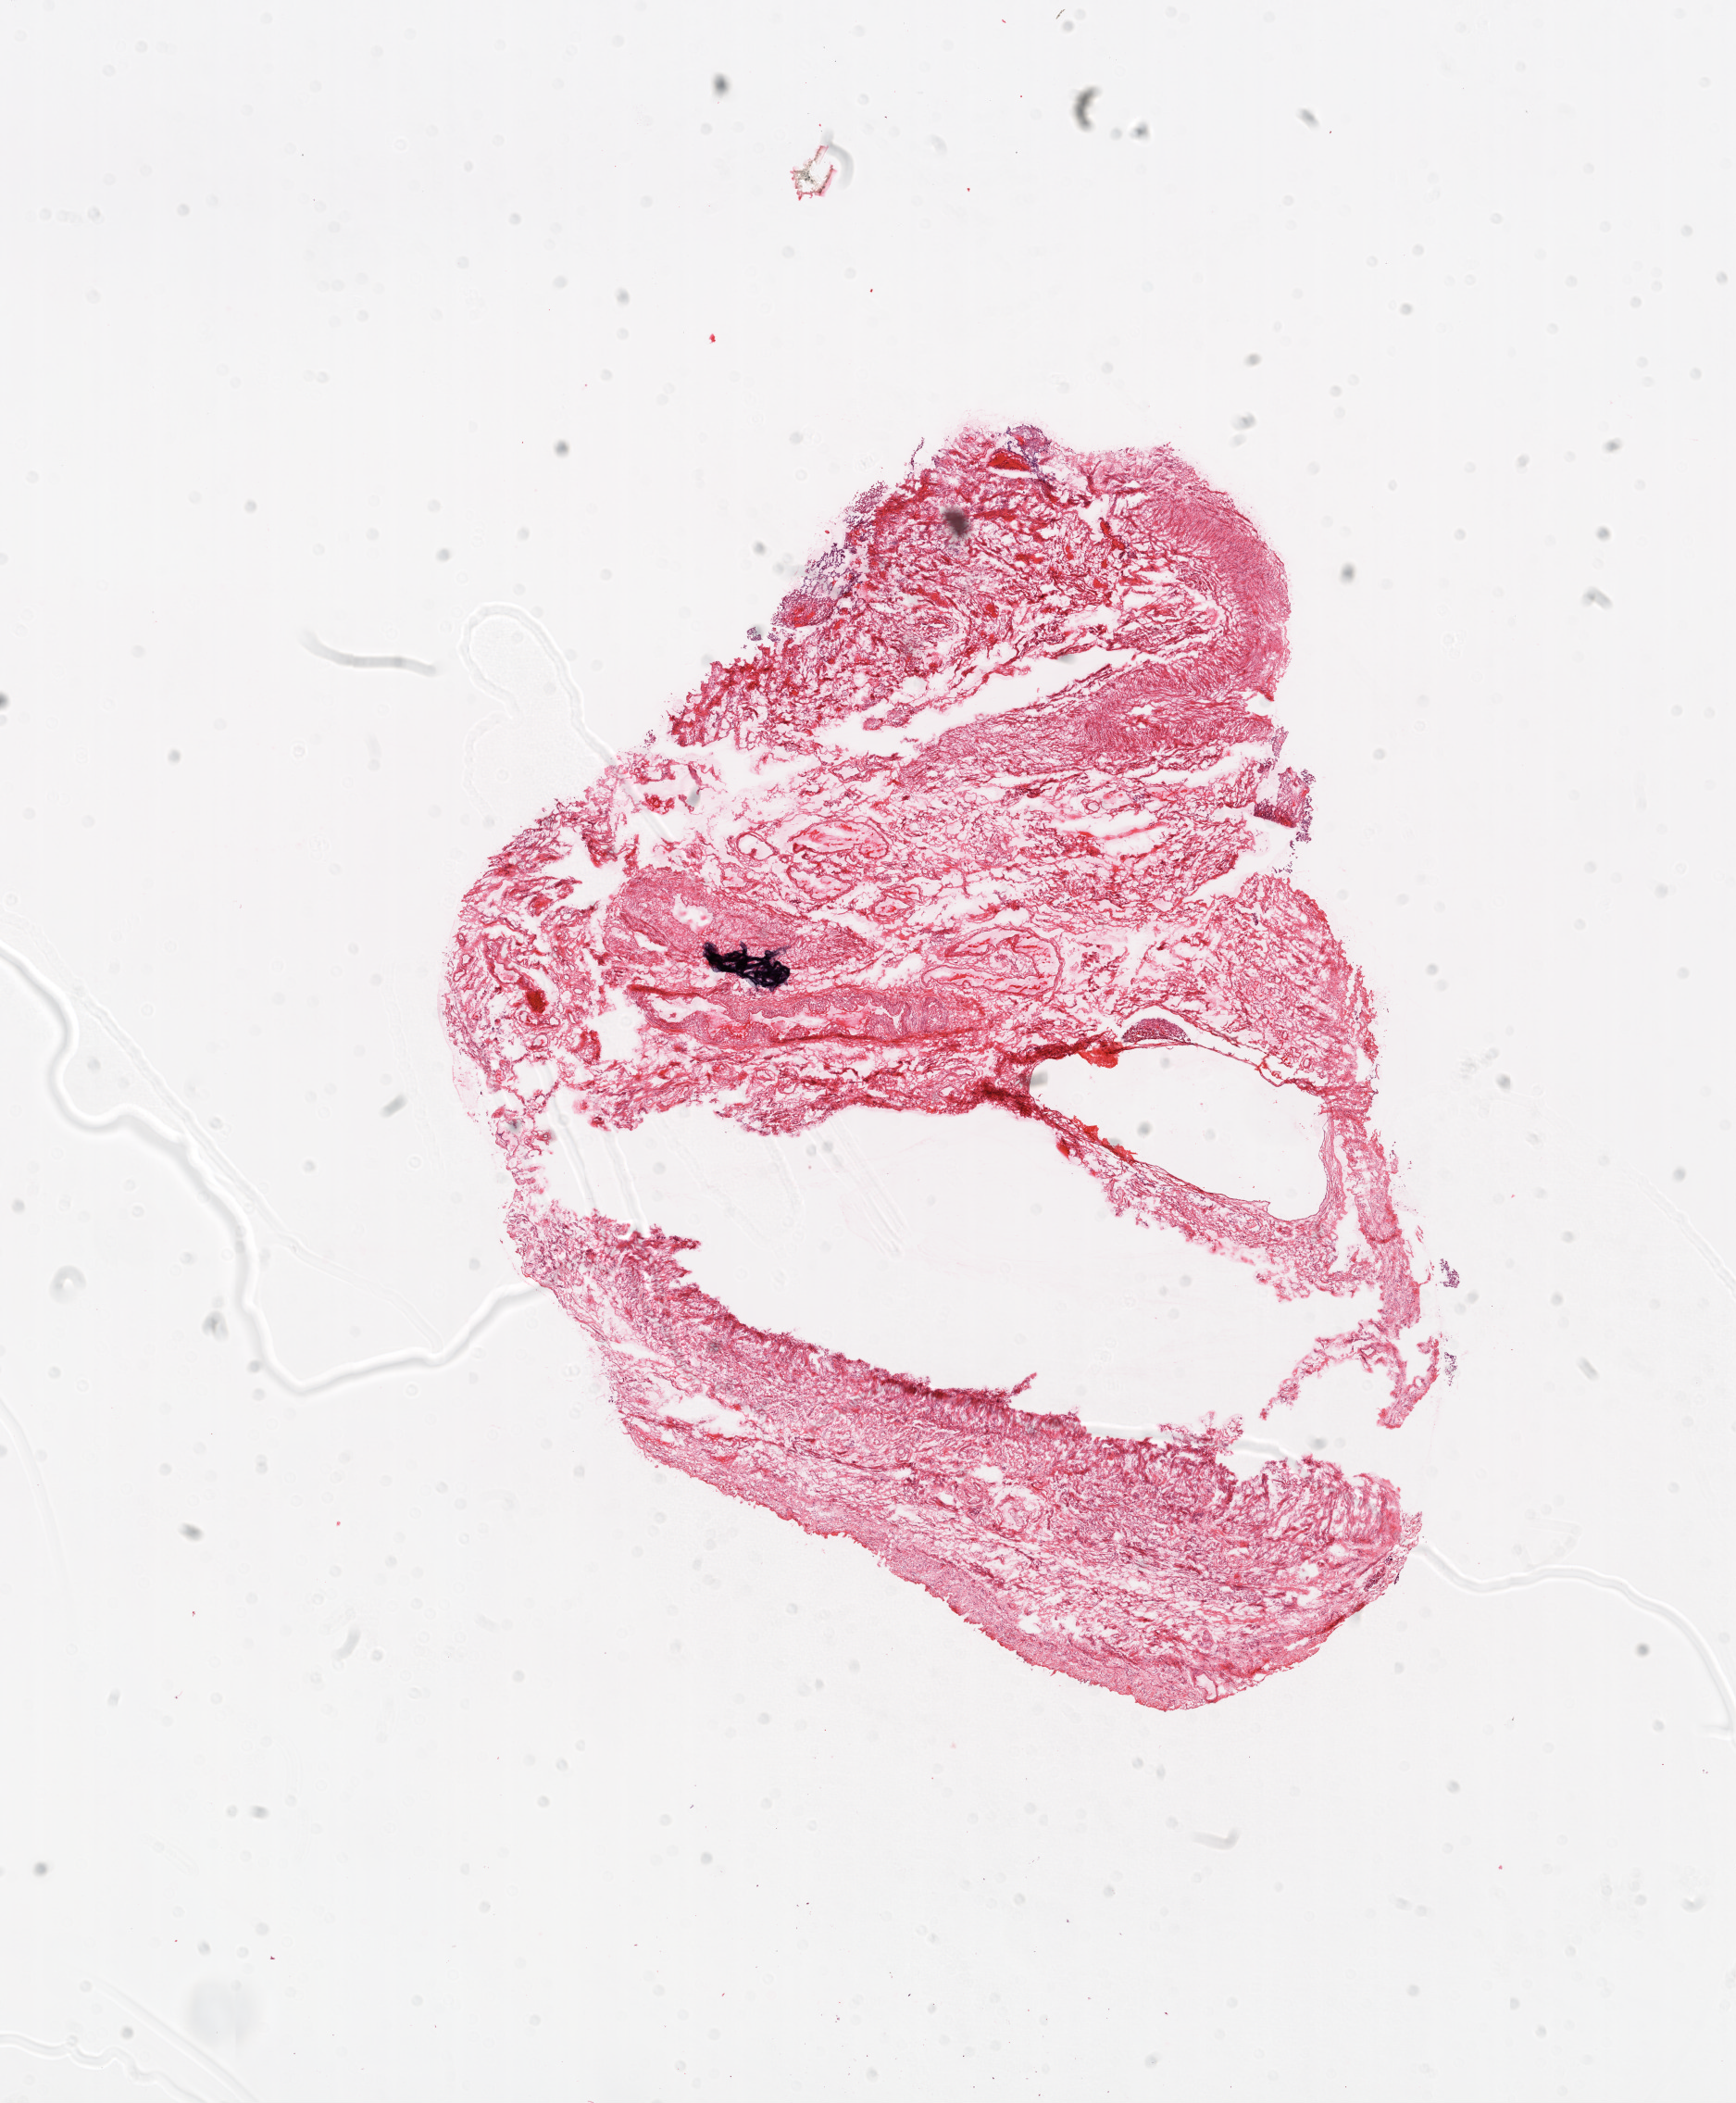
H&E whole-slide image, shown as a low-resolution overview of the whole scanned area (about 15.0 x 18.2 mm, acquisition: 20x scan), frozen section, solid tissue normal (non-tumour tissue) sample from the ovary. Female patient; age at initial diagnosis 67 years.
This section: solid tissue normal (non-tumour) sample from the same patient. Patient diagnosis: Serous cystadenocarcinoma, NOS.